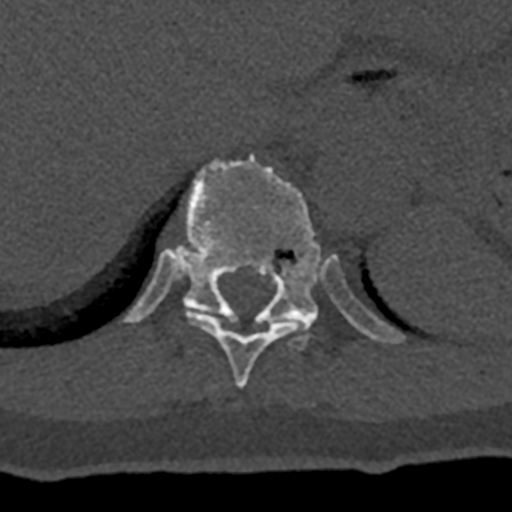
CT including the spine, one axial slice. Slice 574 of 797 in the series (ordered by position). 120 kVp. Bone window (W 1800 / L 400 HU). 0.5 mm slice thickness. 512 × 512 image matrix, field of view 160 × 160 mm. Male patient, age 74 years. From the clinical record (not read from this slice): primary cancer: renal; vertebrae with lytic lesions (as recorded): T10, L1, L2, L3, L4, L5.
Outlined on this slice (semi-automatic segmentation, software-assisted and operator-edited):
- T10 vertebra: bounding box <187,311,310,389> (left, top, right, bottom; pixels)
- T11 vertebra: <124,155,405,351>